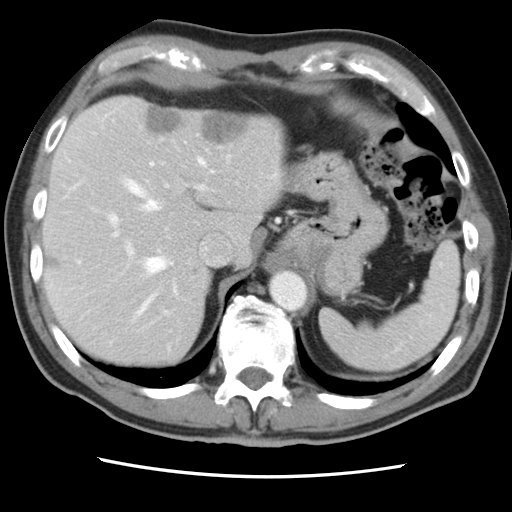
Contrast-enhanced abdominal CT, one axial slice. Position 63 of 83 along the scan axis. 120 kVp. Intravenous contrast given. Soft-tissue window (W 400 / L 40 HU). 5 mm slice thickness. 512 × 512 image matrix, field of view 321 × 321 mm. Male patient, age 69 years. Case-level facts recorded for this patient, not image findings: diagnosis: colorectal cancer liver metastases, imaged before liver resection; multiple liver metastases: yes; largest metastasis: 3.5 cm; disease in both lobes: no.
Annotated regions visible in this slice (expert manual segmentation):
- hepatic veins: bounding box [x1, y1, x2, y2] px = [69, 113, 214, 314]
- liver: [44, 97, 282, 367]
- planned liver remnant (the part of the liver to remain after resection): [44, 144, 211, 367]
- portal vein (with intrahepatic branches): [108, 161, 207, 313]
- liver metastasis: [147, 107, 183, 133]
- liver metastasis: [193, 268, 199, 274]
- liver metastasis: [203, 115, 250, 143]